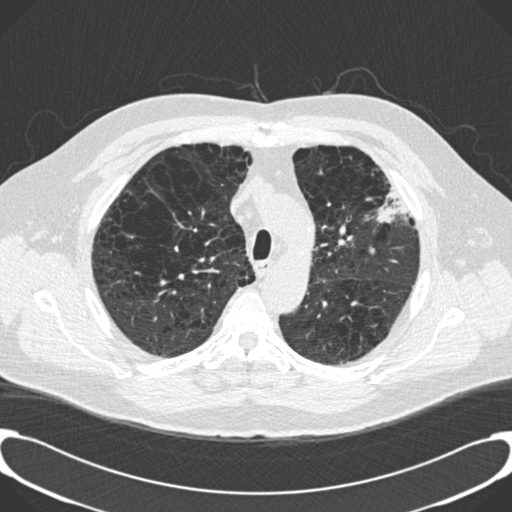
Low-dose screening chest CT, one axial slice; position 148 of 189 along the scan axis; reconstruction kernel B30f; 120 kVp; lung window (W 1500 / L -600 HU); 2 mm slice thickness; 512 × 512 image matrix, field of view 380 × 380 mm.
Outlined on this slice (manually delineated by an expert):
- lesion 1 (tumor, upper lobe of left lung): bounding box (x1, y1, x2, y2) in pixels: (377, 185, 411, 223)